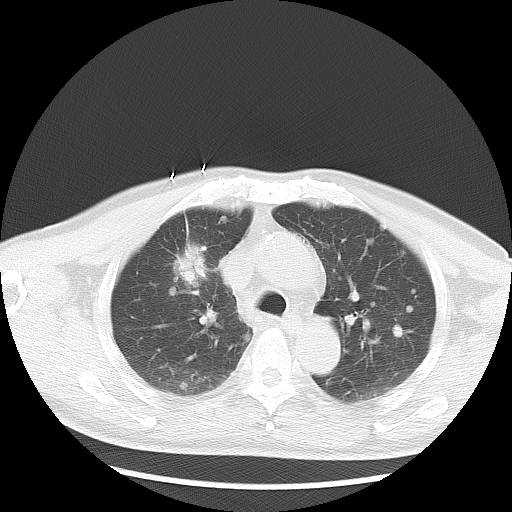
Chest CT, one axial slice. Slice 20 of 36 in the series (ordered by position). 120 kVp. Lung window (W 1500 / L -600 HU). 512 × 512 image matrix. Patient: male, 57 years. From the clinical record (not read from this slice): clinical TNM (as recorded): T2 N3 M1a.
Outlined on this slice (bounding box drawn by a radiologist):
- lung tumour (recorded histology: adenocarcinoma): bounding box (x1, y1, x2, y2) in pixels: (172, 239, 207, 289)